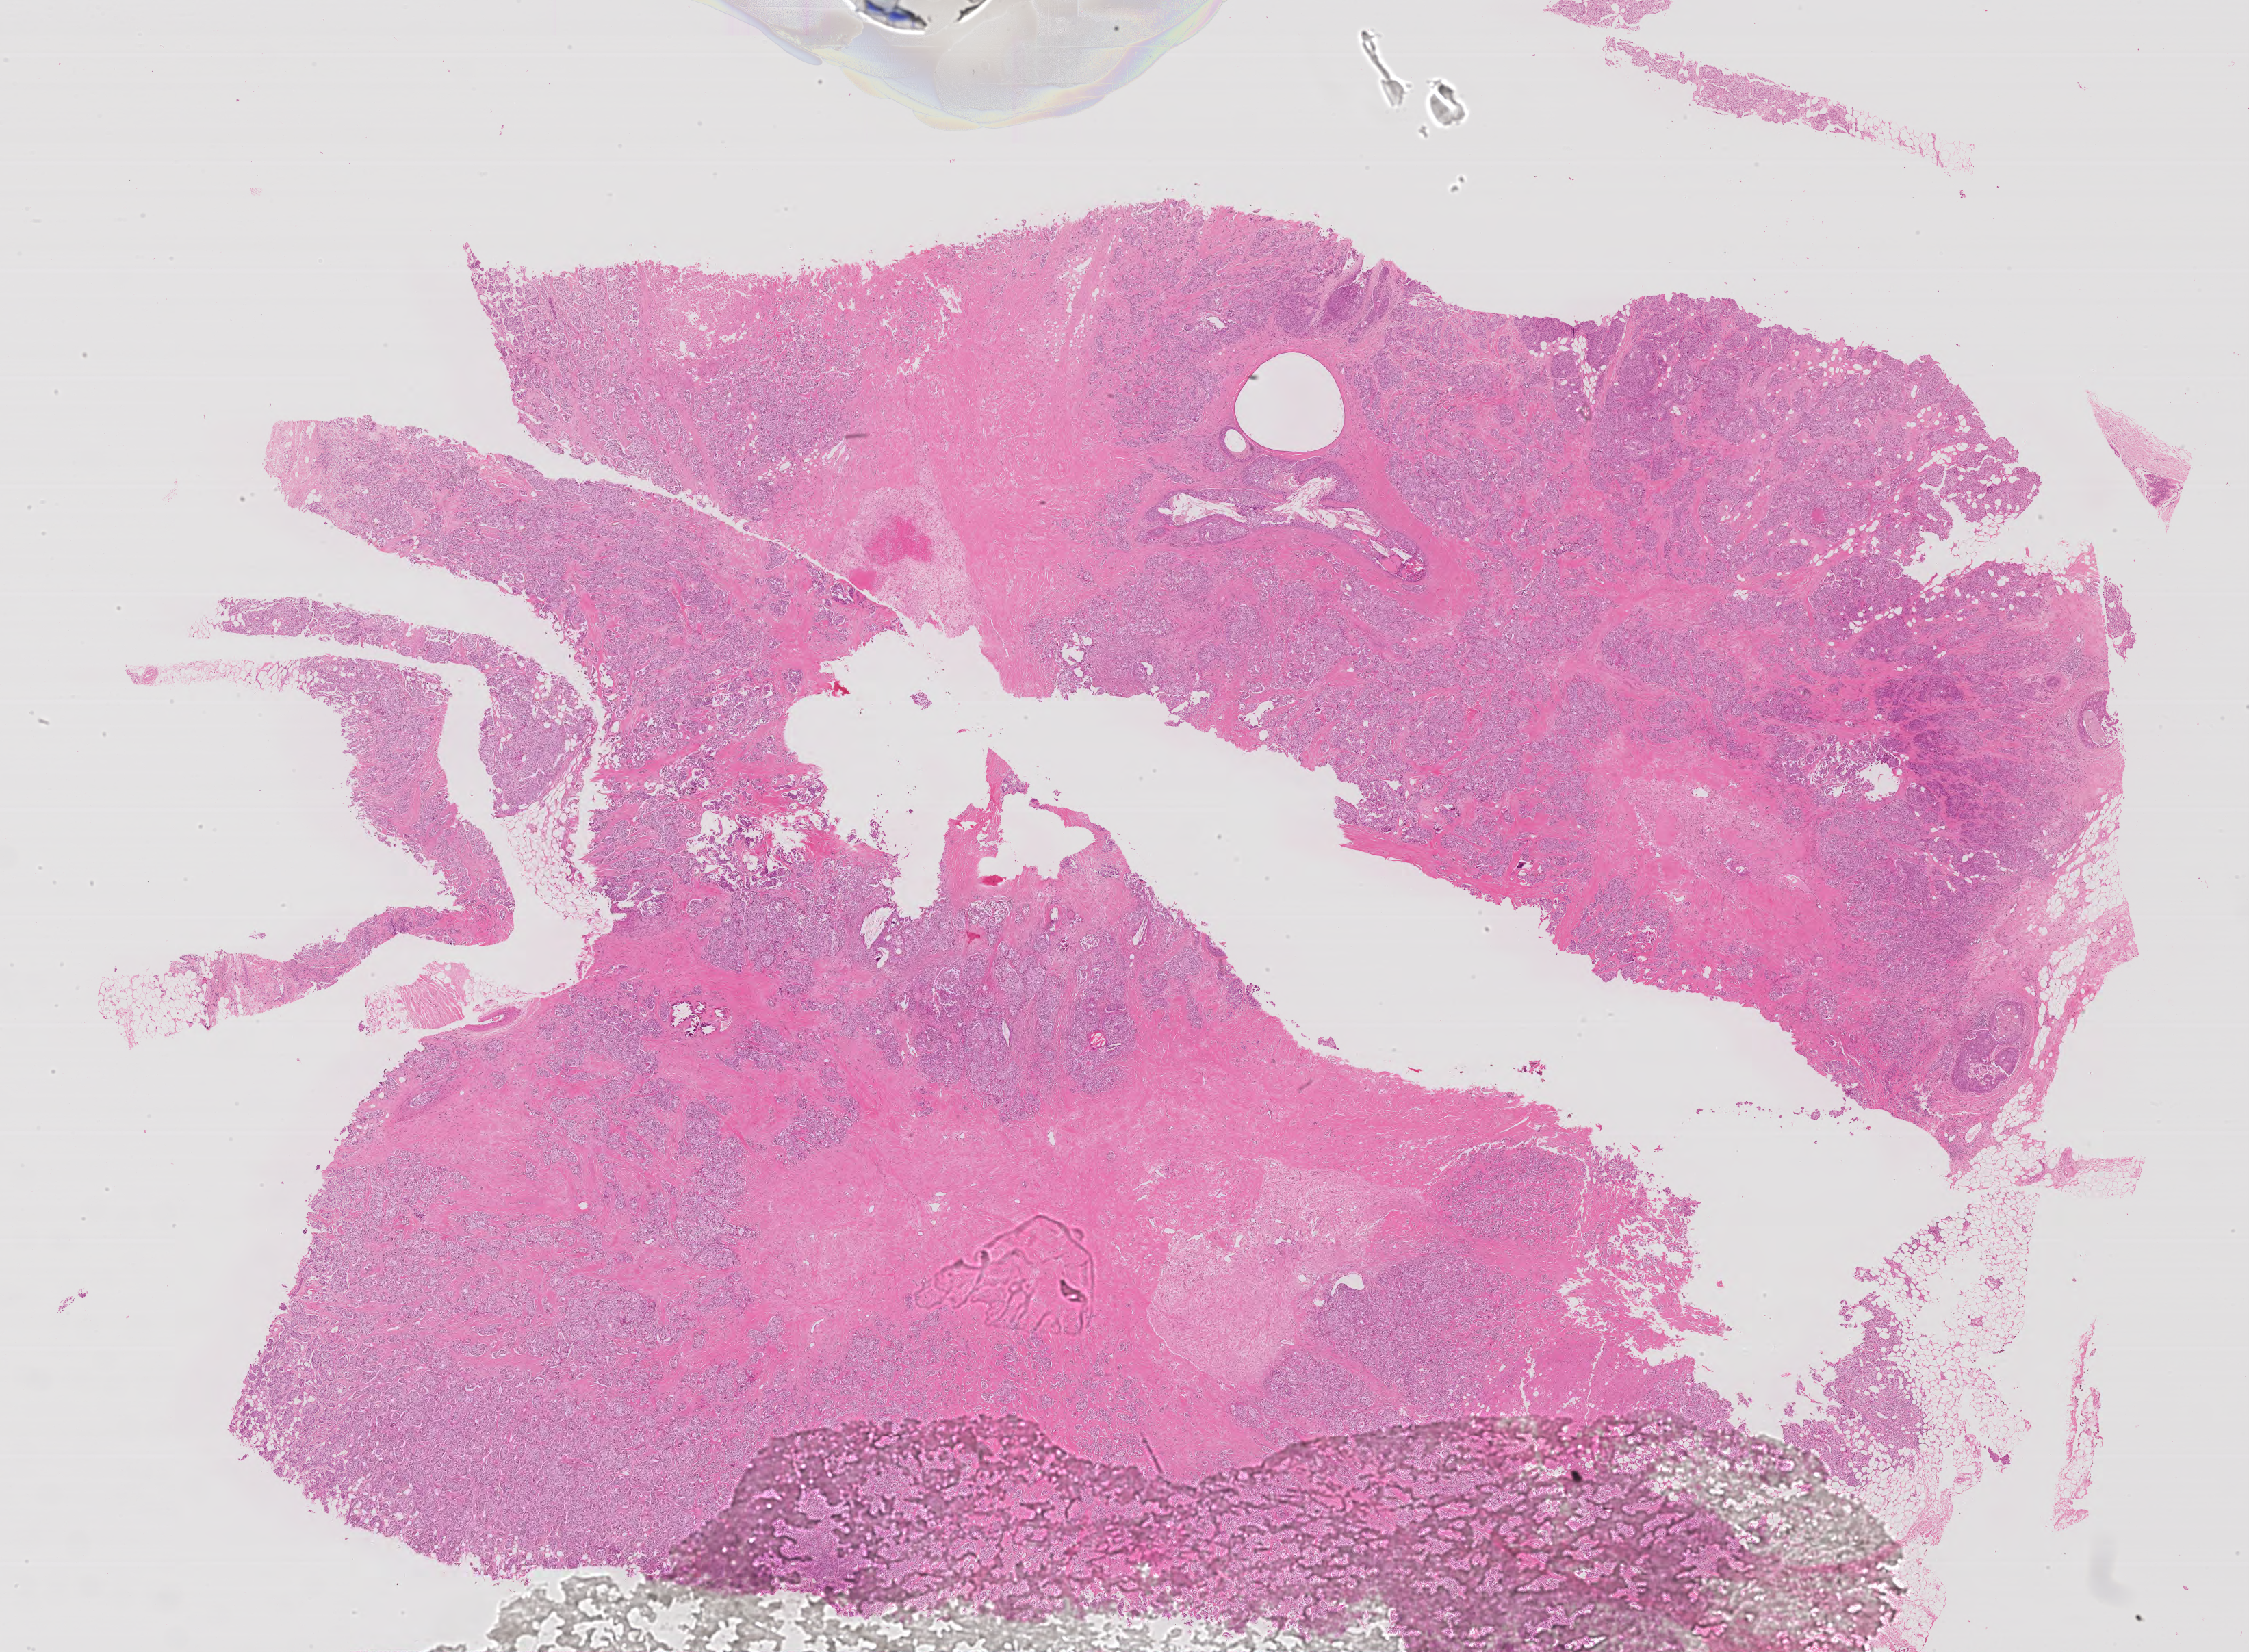
Whole-slide histology image, Hematoxylin and eosin (H&E) stained, whole scanned area (about 26.3 x 19.3 mm, from a 40x scan) shown as a low-resolution overview. FFPE section. Sample: primary tumour, breast. Female patient; age at initial diagnosis 62 years.
Pathologic diagnosis: Infiltrating duct carcinoma, NOS. TNM: T2 N1a M0. AJCC pathologic stage: IIB (7th edition).